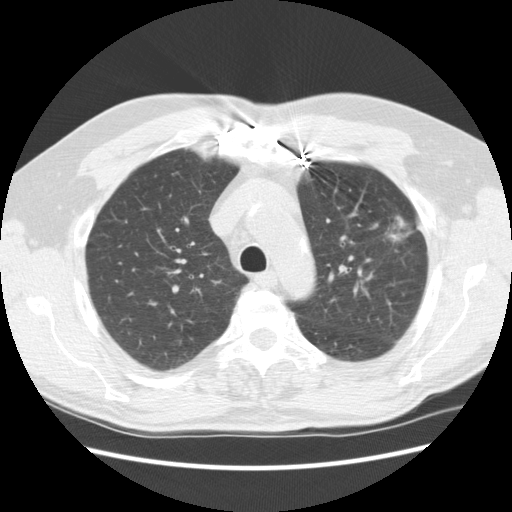
Axial slice from a low-dose chest CT screening exam, baseline annual screen, lung window (W 1500 / L -600 HU), 2.5 mm slice thickness, 120 kVp, slice 179 of 231 in the series, 512 × 512 image matrix. Male, age 72 years at enrolment. Former smoker at enrolment.
Expert reader's lesion annotation, bounding box (x1, y1, x2, y2) in pixels: (344, 194, 429, 260). Reader record for this screening exam (exam-level; its link to the box is not recorded): non-calcified nodule or mass ≥4 mm, left upper lobe, 25 × 18 mm, spiculated (stellate) margins, soft tissue attenuation. Lung cancer was diagnosed 35 days after this screen: adenocarcinoma, NOS, left upper lobe, well differentiated (G1), stage IIIB (AJCC 6th edition), 25 mm at pathology.